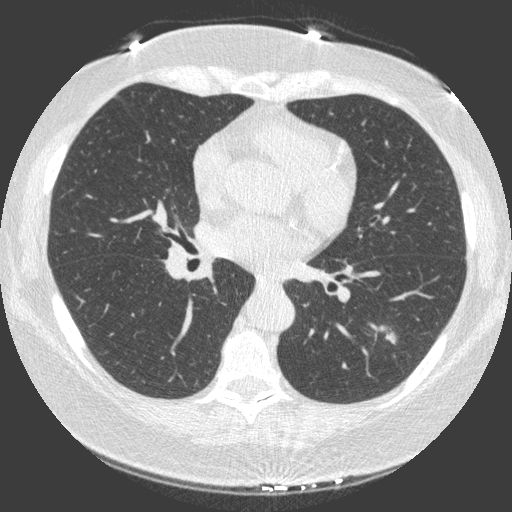
Low-dose screening chest CT, one axial slice; slice 82 of 149 in the series (ordered by position); lung window (W 1500 / L -600 HU); 512 × 512 image matrix, field of view 330 × 330 mm.
Annotated regions visible in this slice (outlined manually by an expert reader):
- lesion 1 (tumor, lower lobe of left lung): box from (x=386, y=333) to (x=395, y=344) px